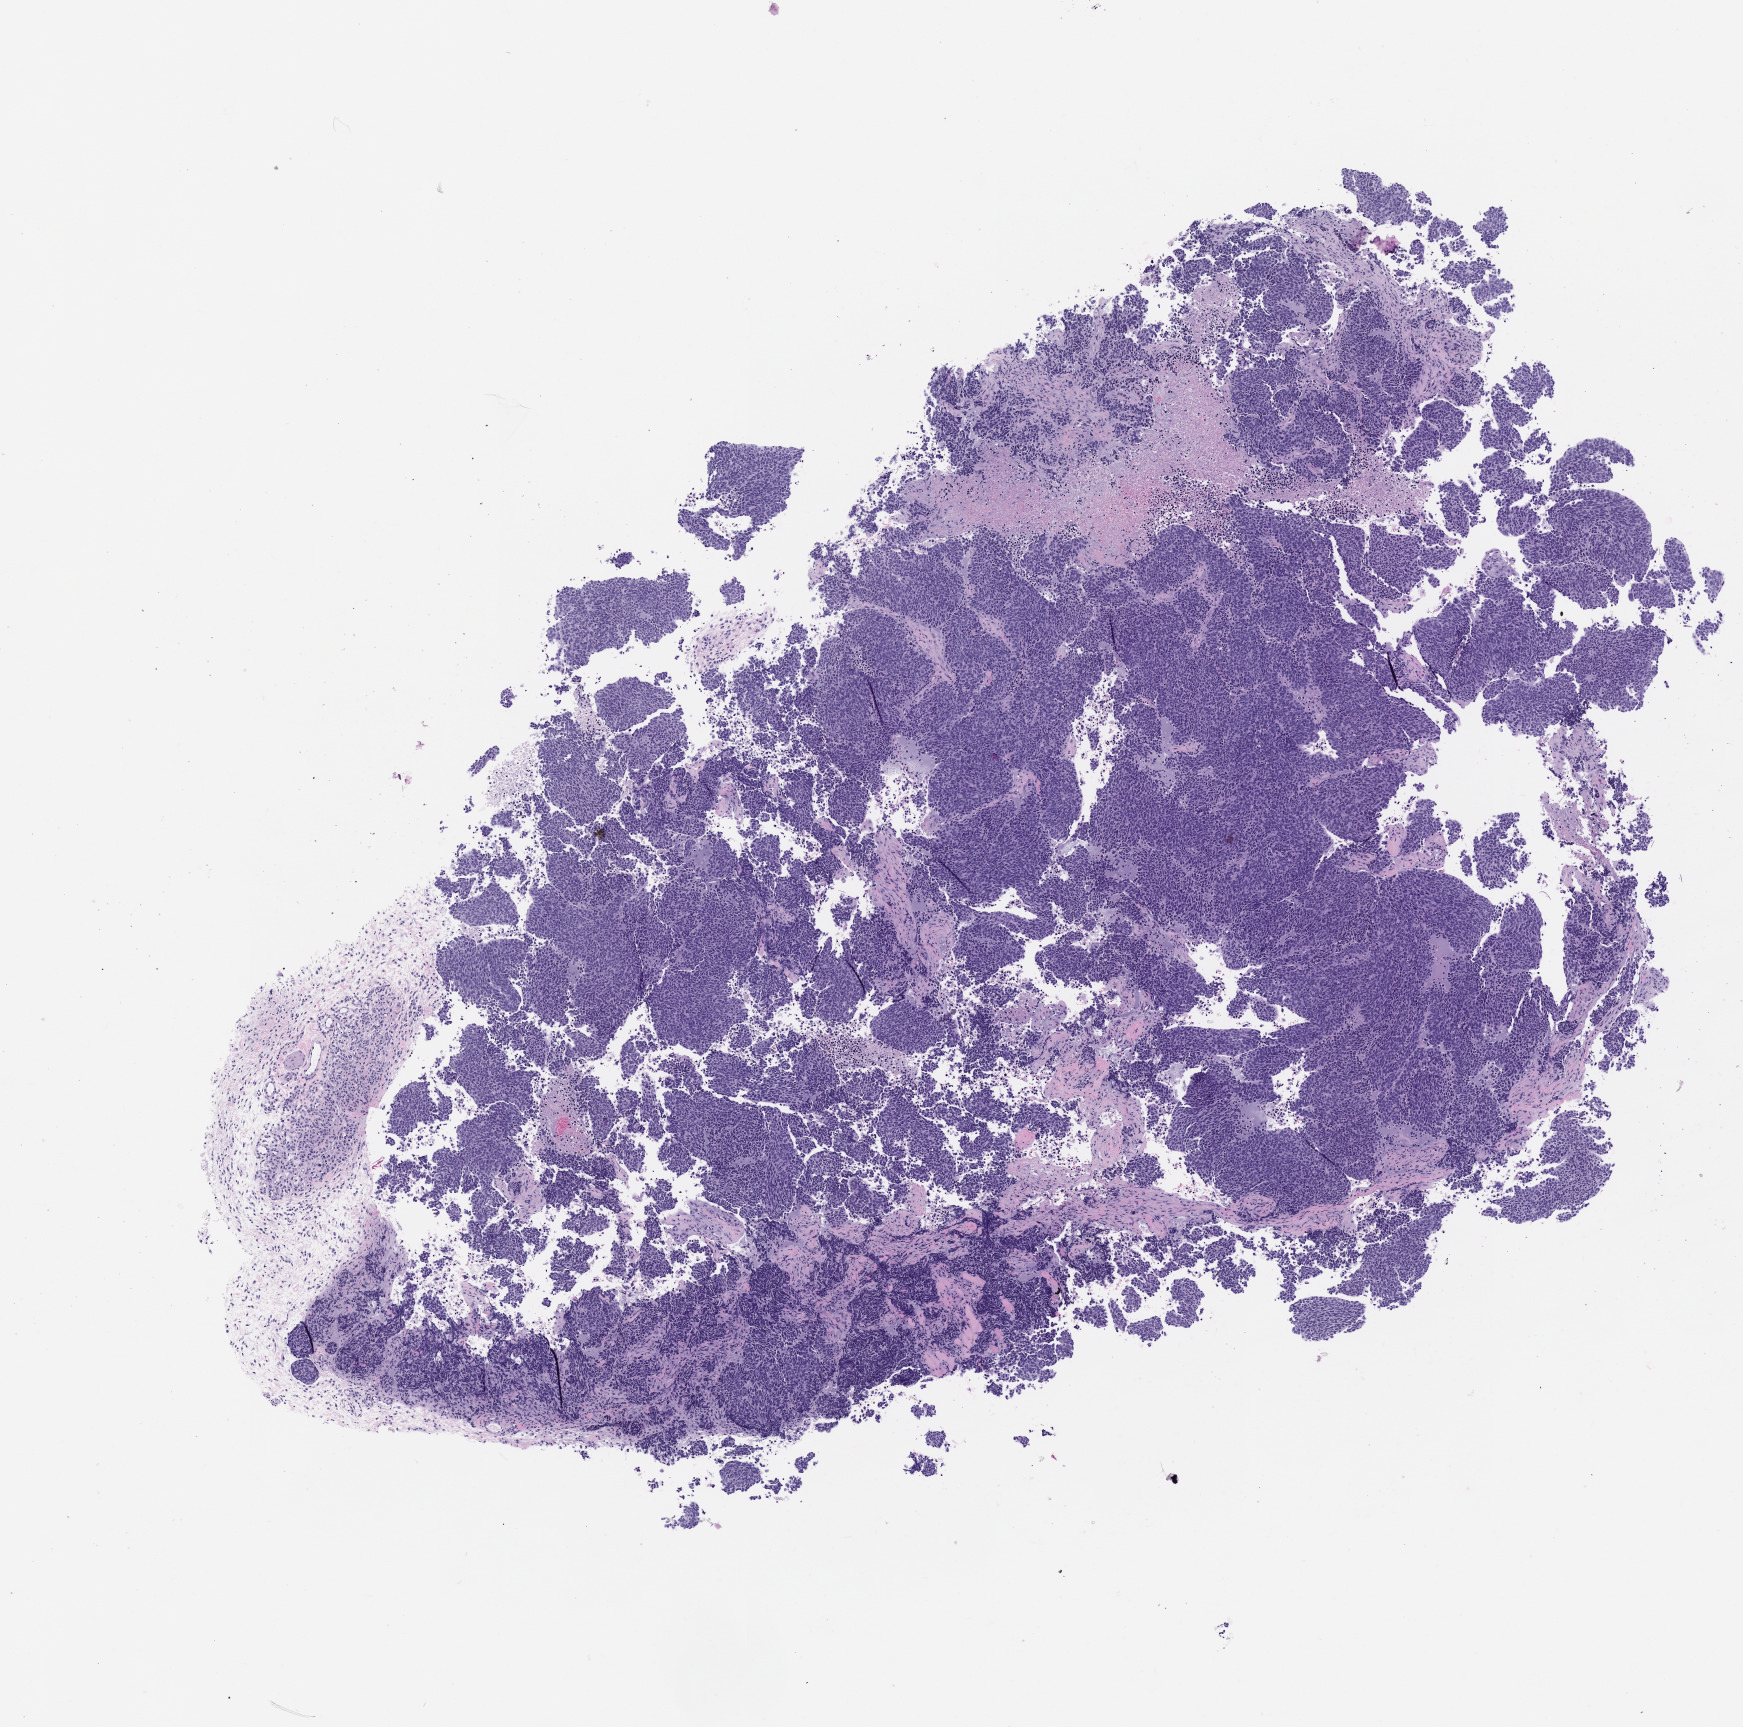
Whole-slide image, H&E: patient-derived xenograft (human tumor grown in a mouse) — whole scanned area (about 7.0 x 6.9 mm) shown as a low-resolution overview. FFPE section. Tumor site category: lung.
Originating patient diagnosis: Lung Adenocarcinoma.